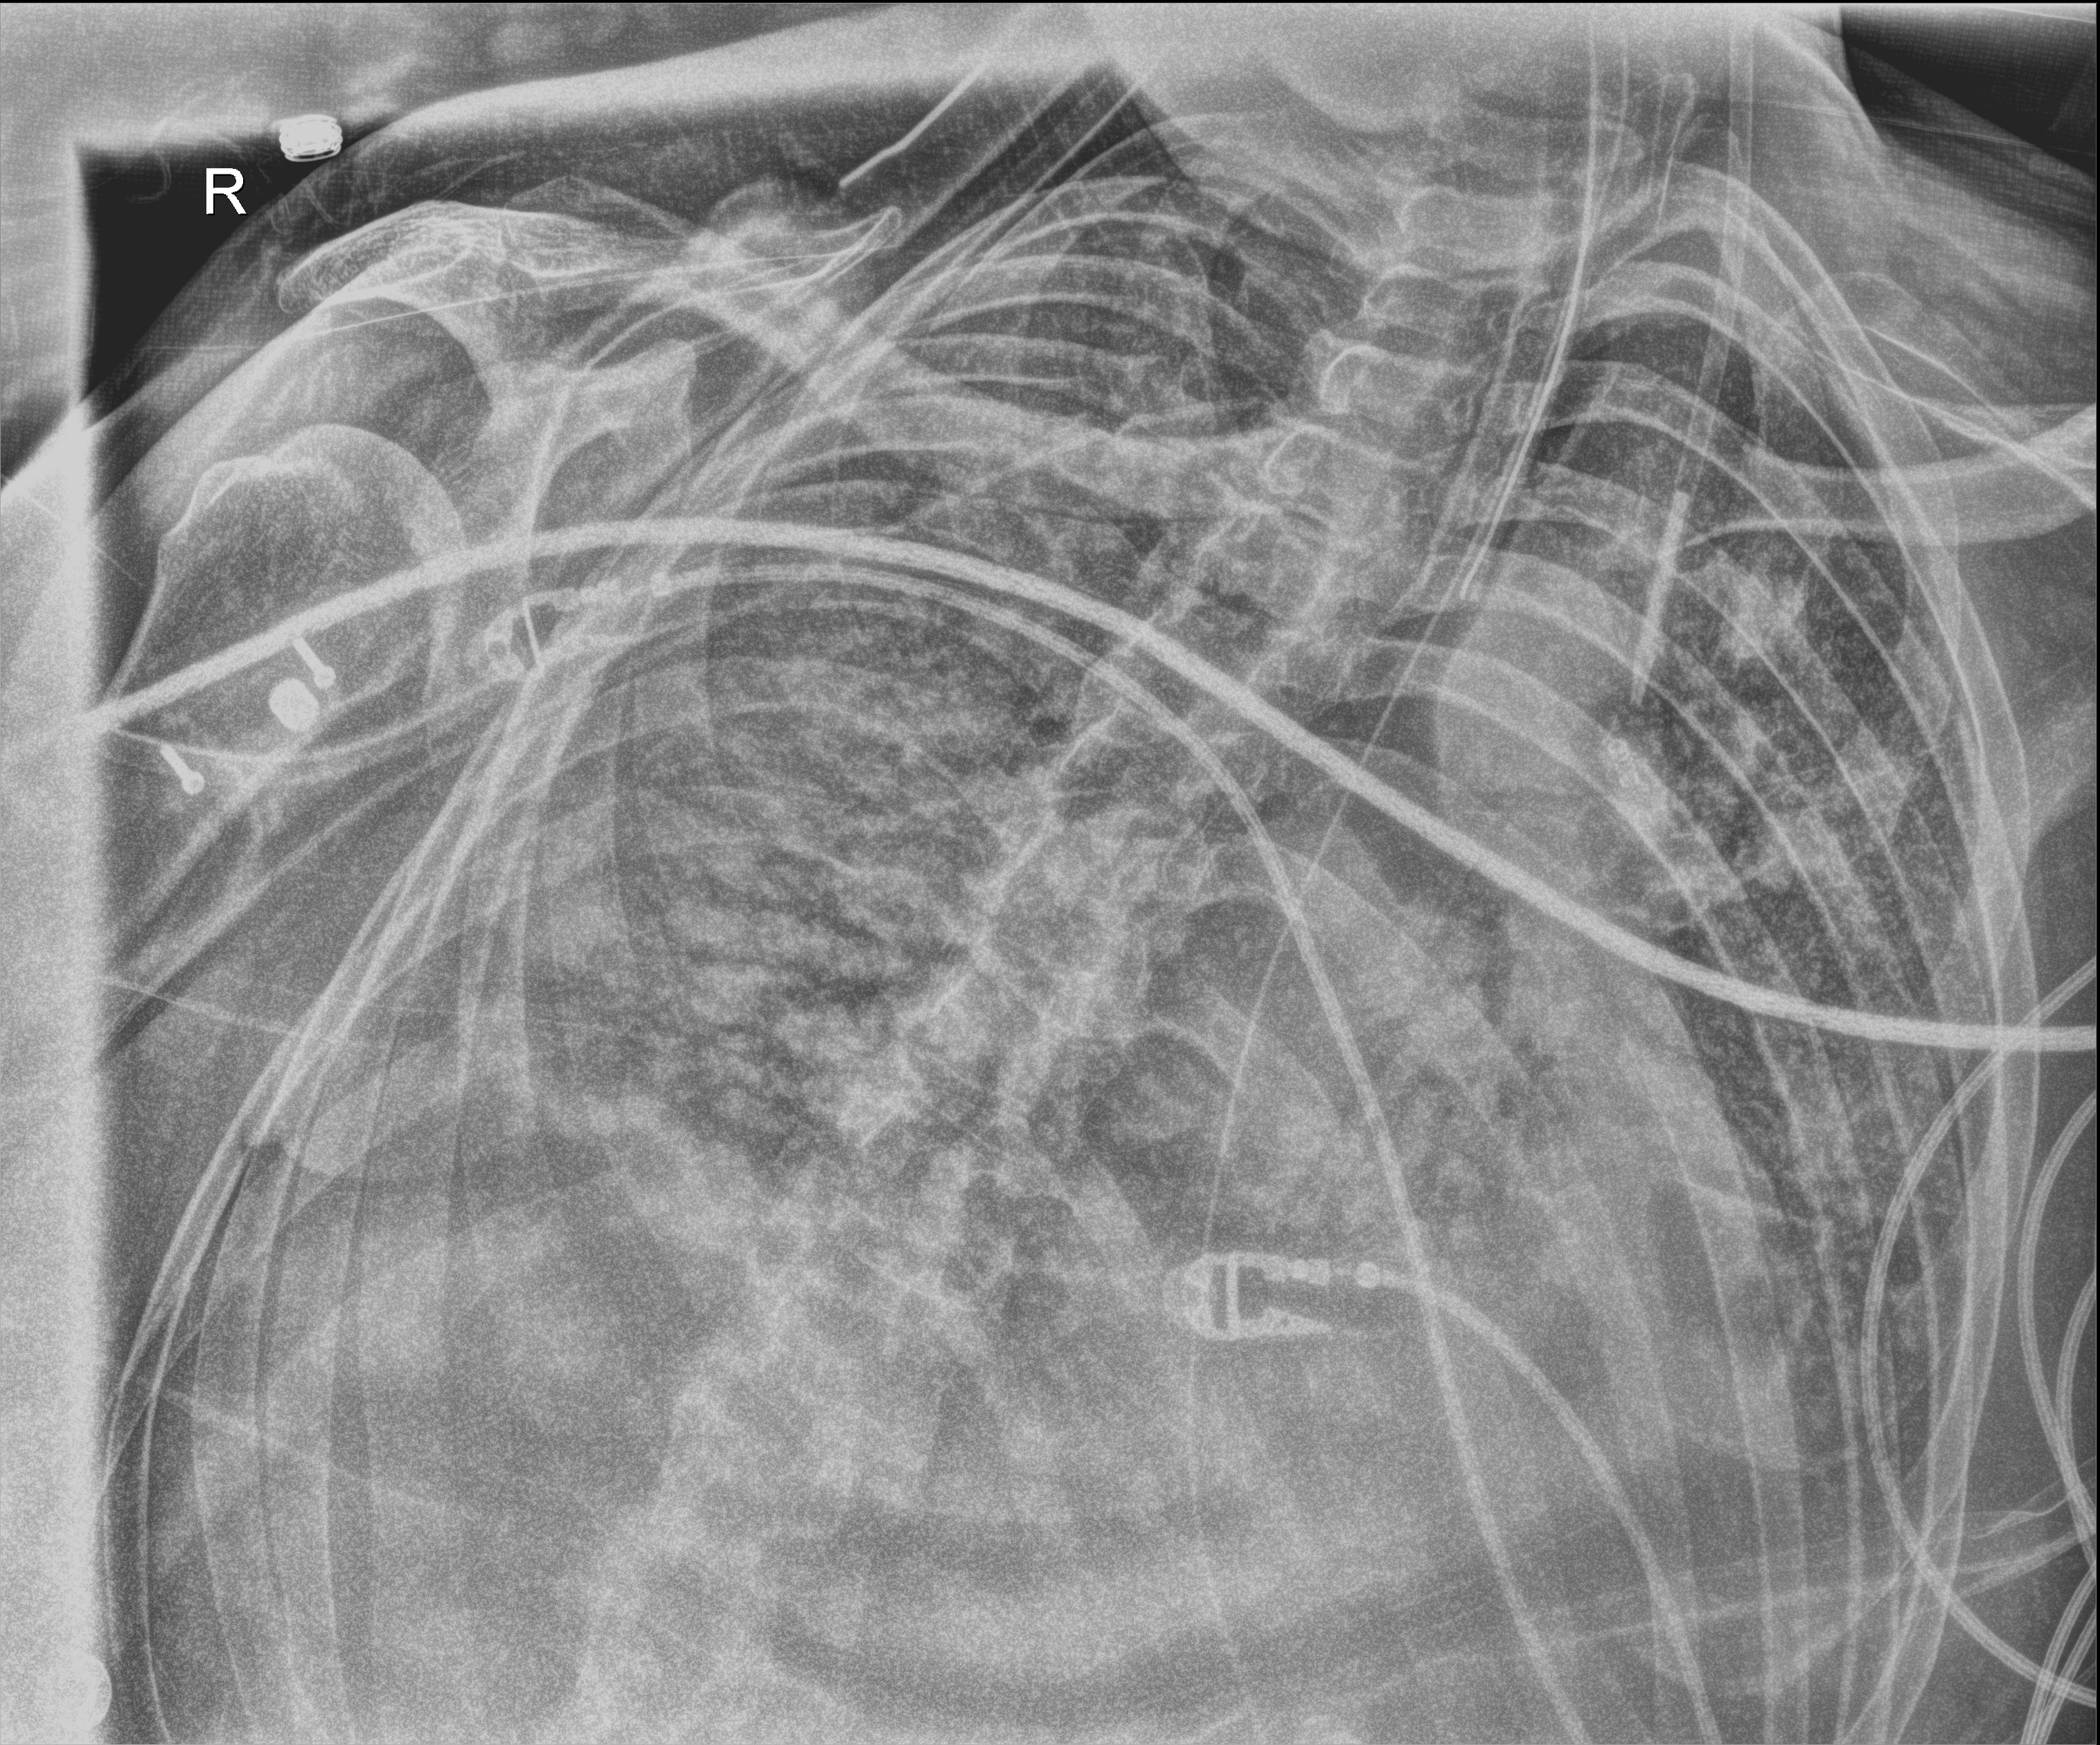
Chest X-ray (portable), anteroposterior (AP) projection. Male patient hospitalised with COVID-19, age 18–59 years.
Hospital-stay facts (about this admission, not read from this image; timing relative to this image not recorded): diabetes (admission record): no.